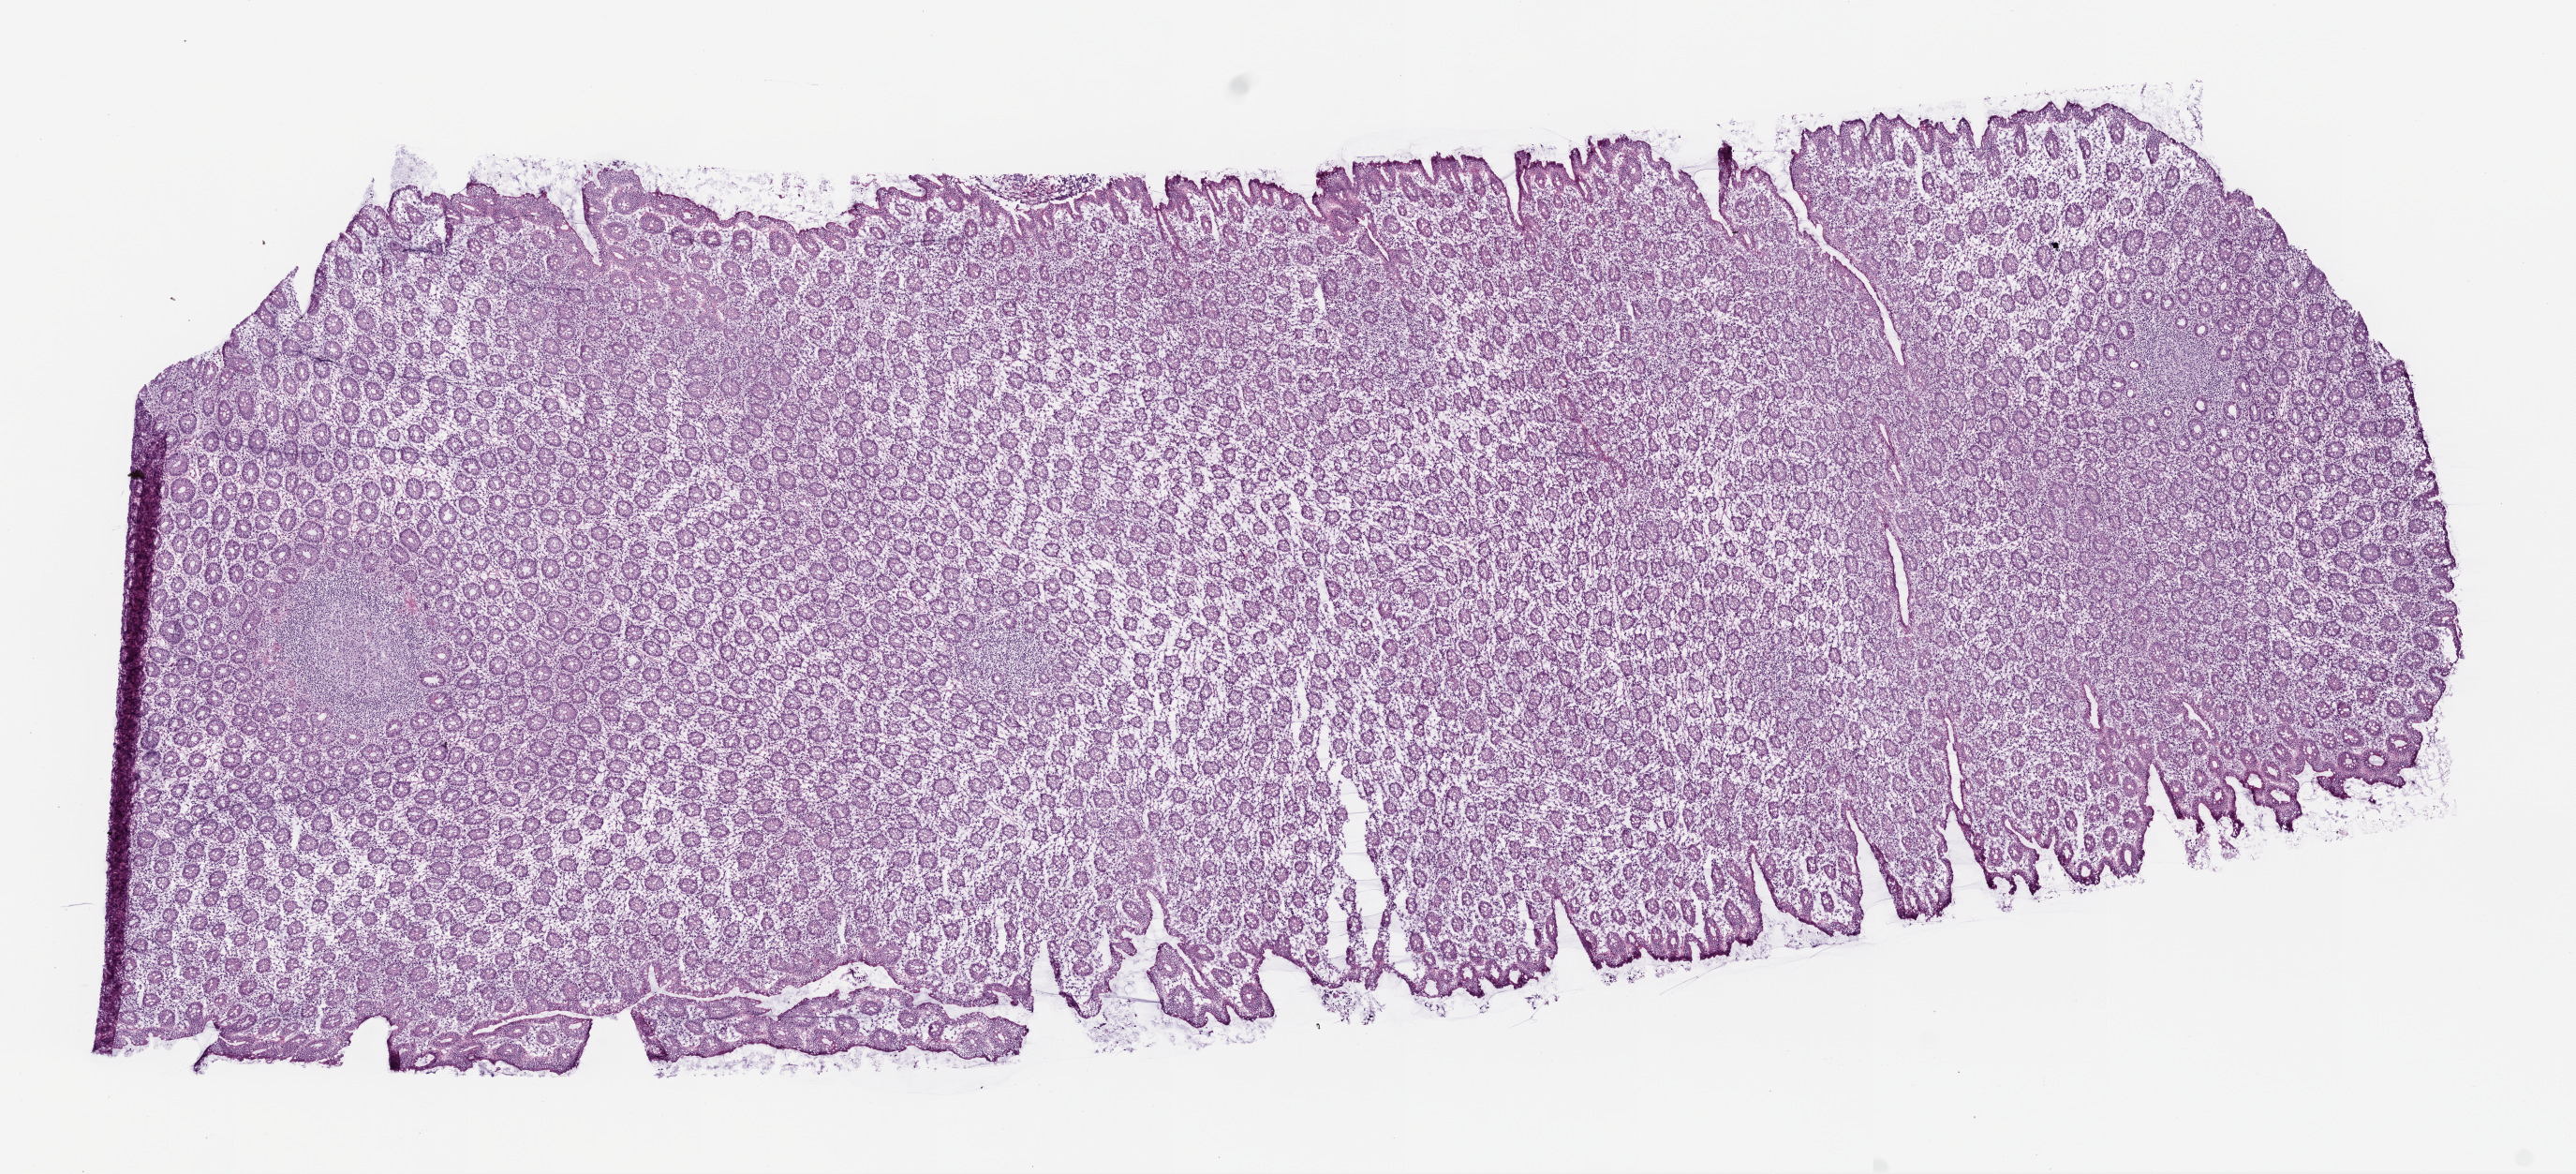
Whole-slide histology image, H&E, shown as a low-resolution overview of the whole scanned area (about 11.0 x 5.0 mm); frozen section from the top of the tissue portion; sample: solid tissue normal (non-tumour tissue), colon. Male patient.
This section: solid tissue normal (non-tumour) sample from the same patient. Patient diagnosis: Adenocarcinoma, NOS (ascending colon).